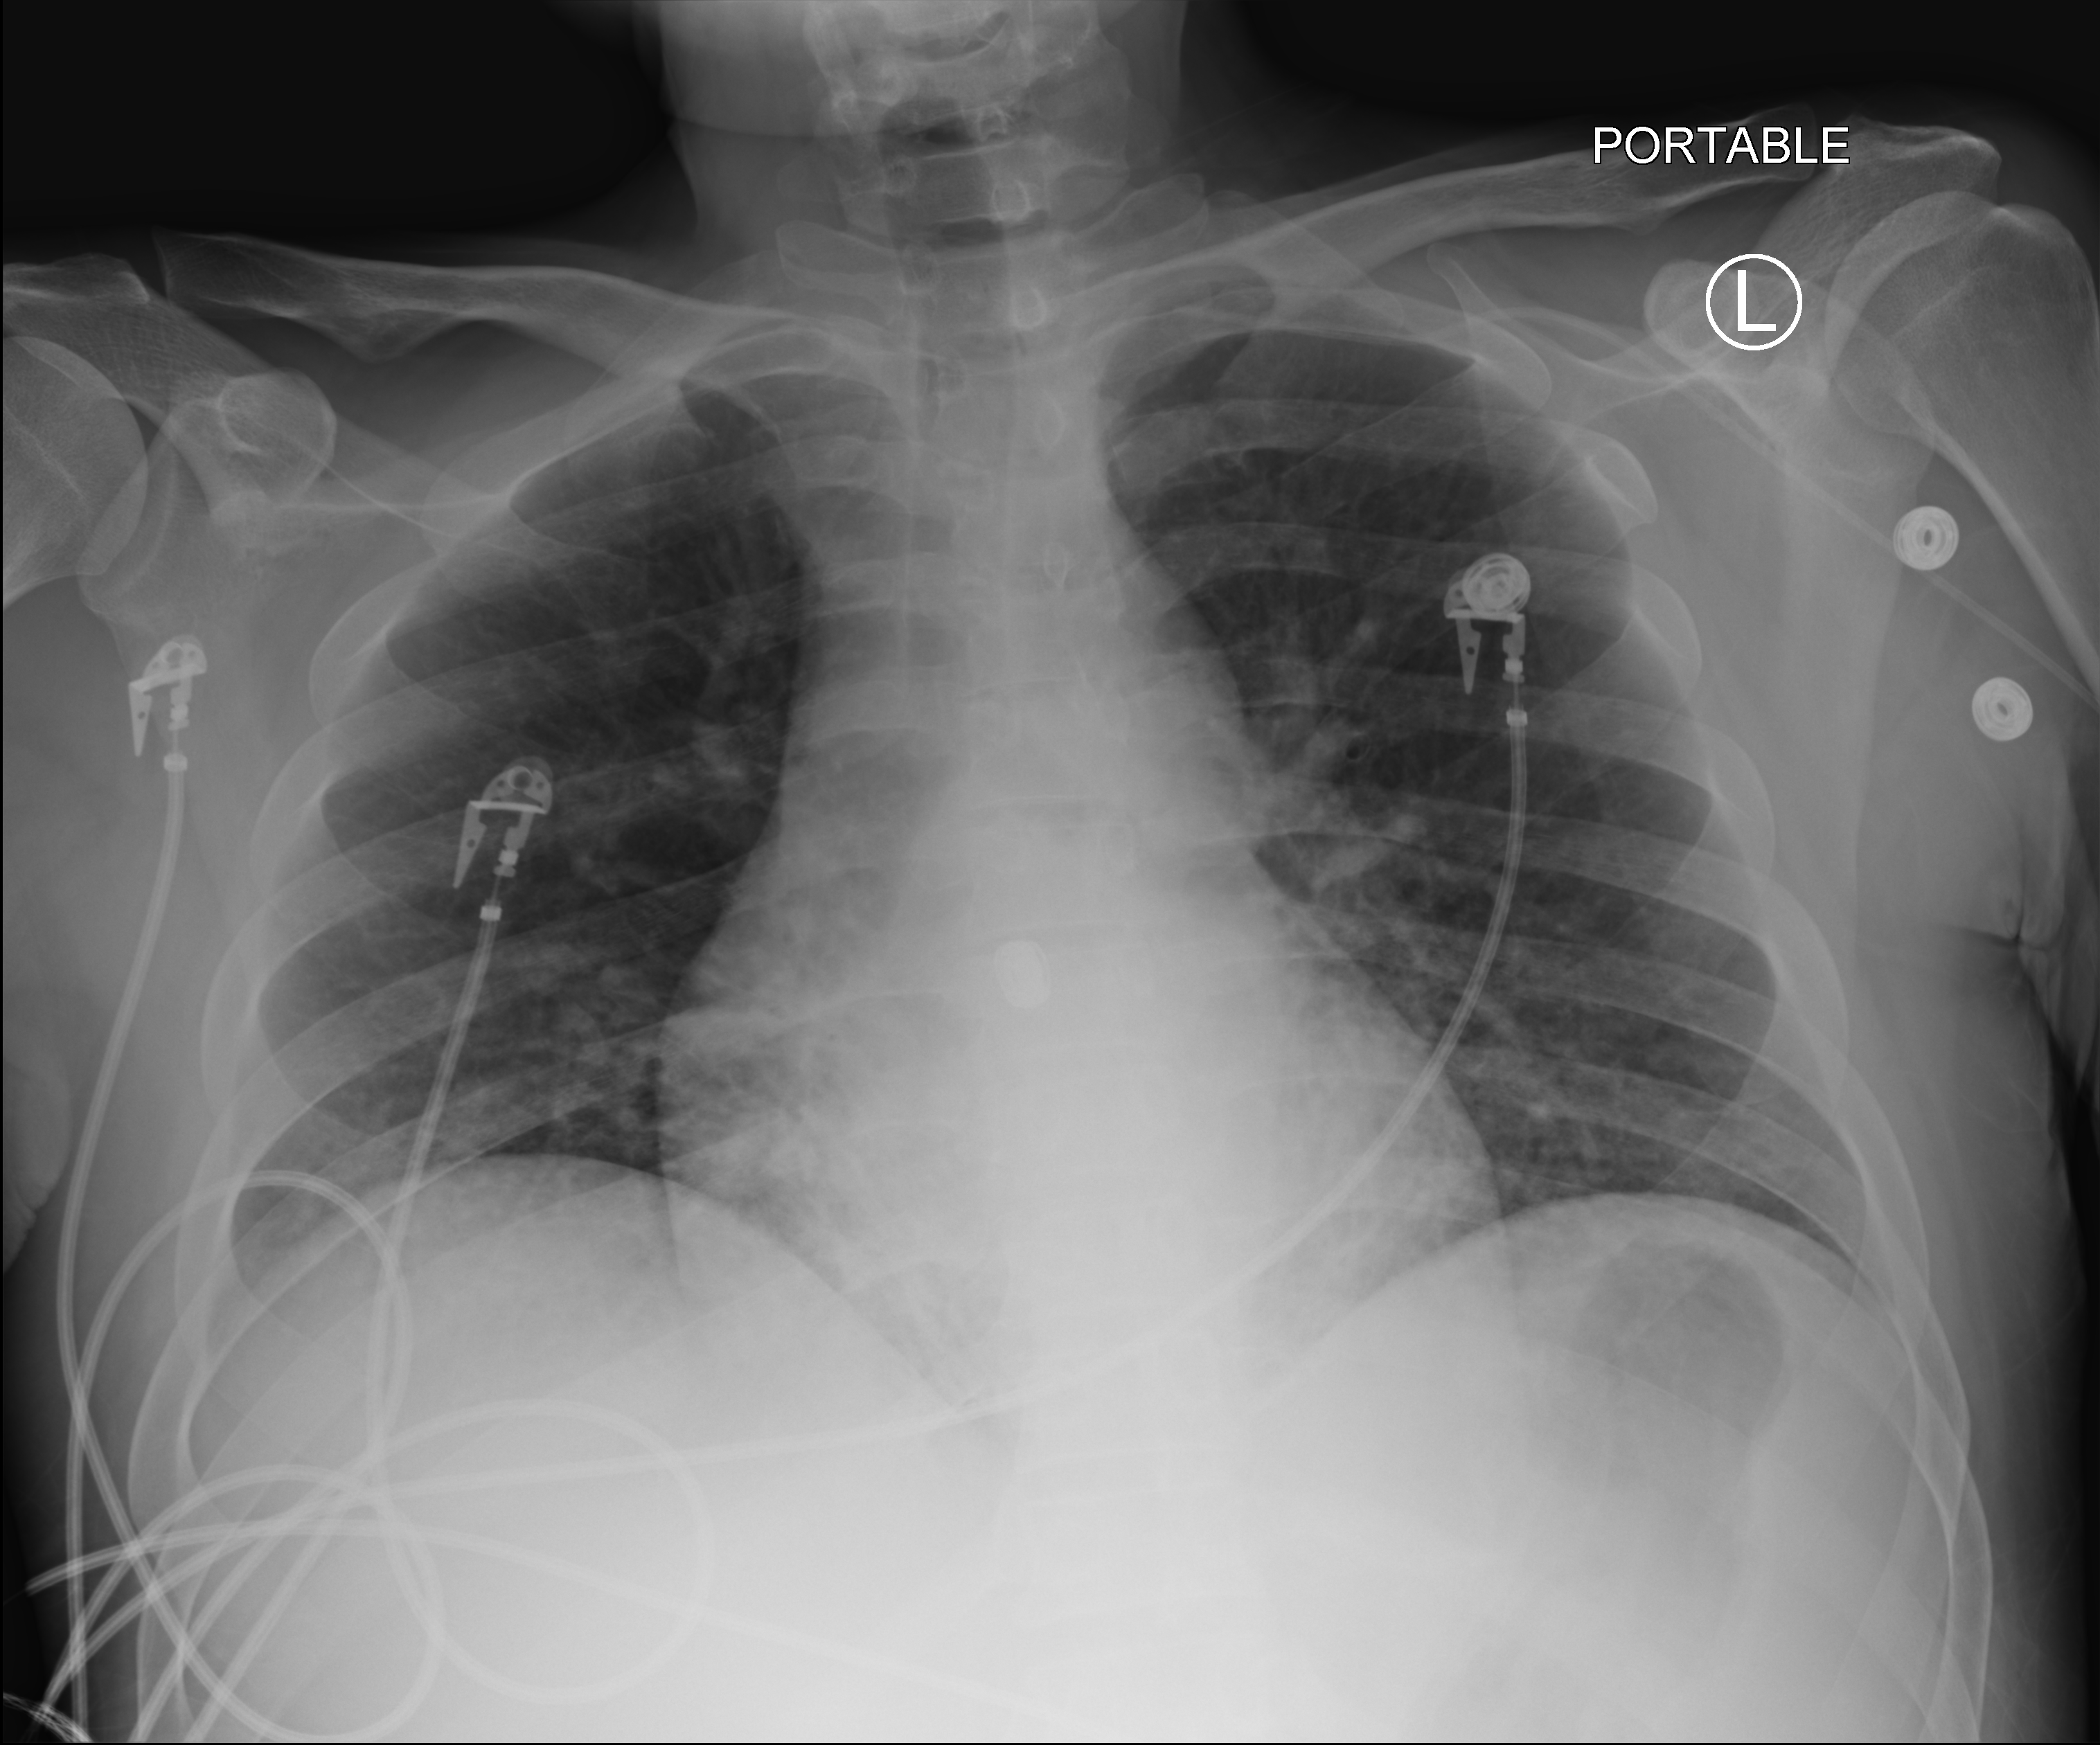
Bedside chest radiograph (computed radiography), anteroposterior (AP) projection. Male patient hospitalised with COVID-19, age 18–59 years.
Admission-level facts for this patient (not findings on this image; timing relative to this image not recorded): admitted to intensive care during this hospital stay: yes.